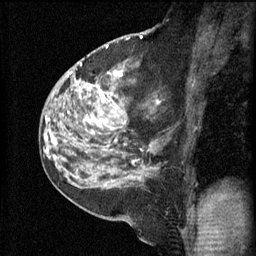
Breast MRI (dynamic contrast-enhanced), one sagittal slice; position 34 of 60 along the scan axis; 3 images stored at this slice position (order not interpretable as contrast timing); 1.5 T; TE 4.2 ms, TR 11 ms; 2.3 mm slice thickness; 256 × 256 image matrix, field of view 180 × 180 mm. Female patient, age 52 years.
Outlined on this slice (semi-automatically segmented with operator editing):
- analysis volume of interest (the breast-tissue region the enhancement analysis was run in; not a lesion): bounding box <86,76,161,157> (left, top, right, bottom; pixels)
- tumour enhancement mask (voxels above the 70 % enhancement threshold inside the analysis volume of interest): <104,76,122,125>